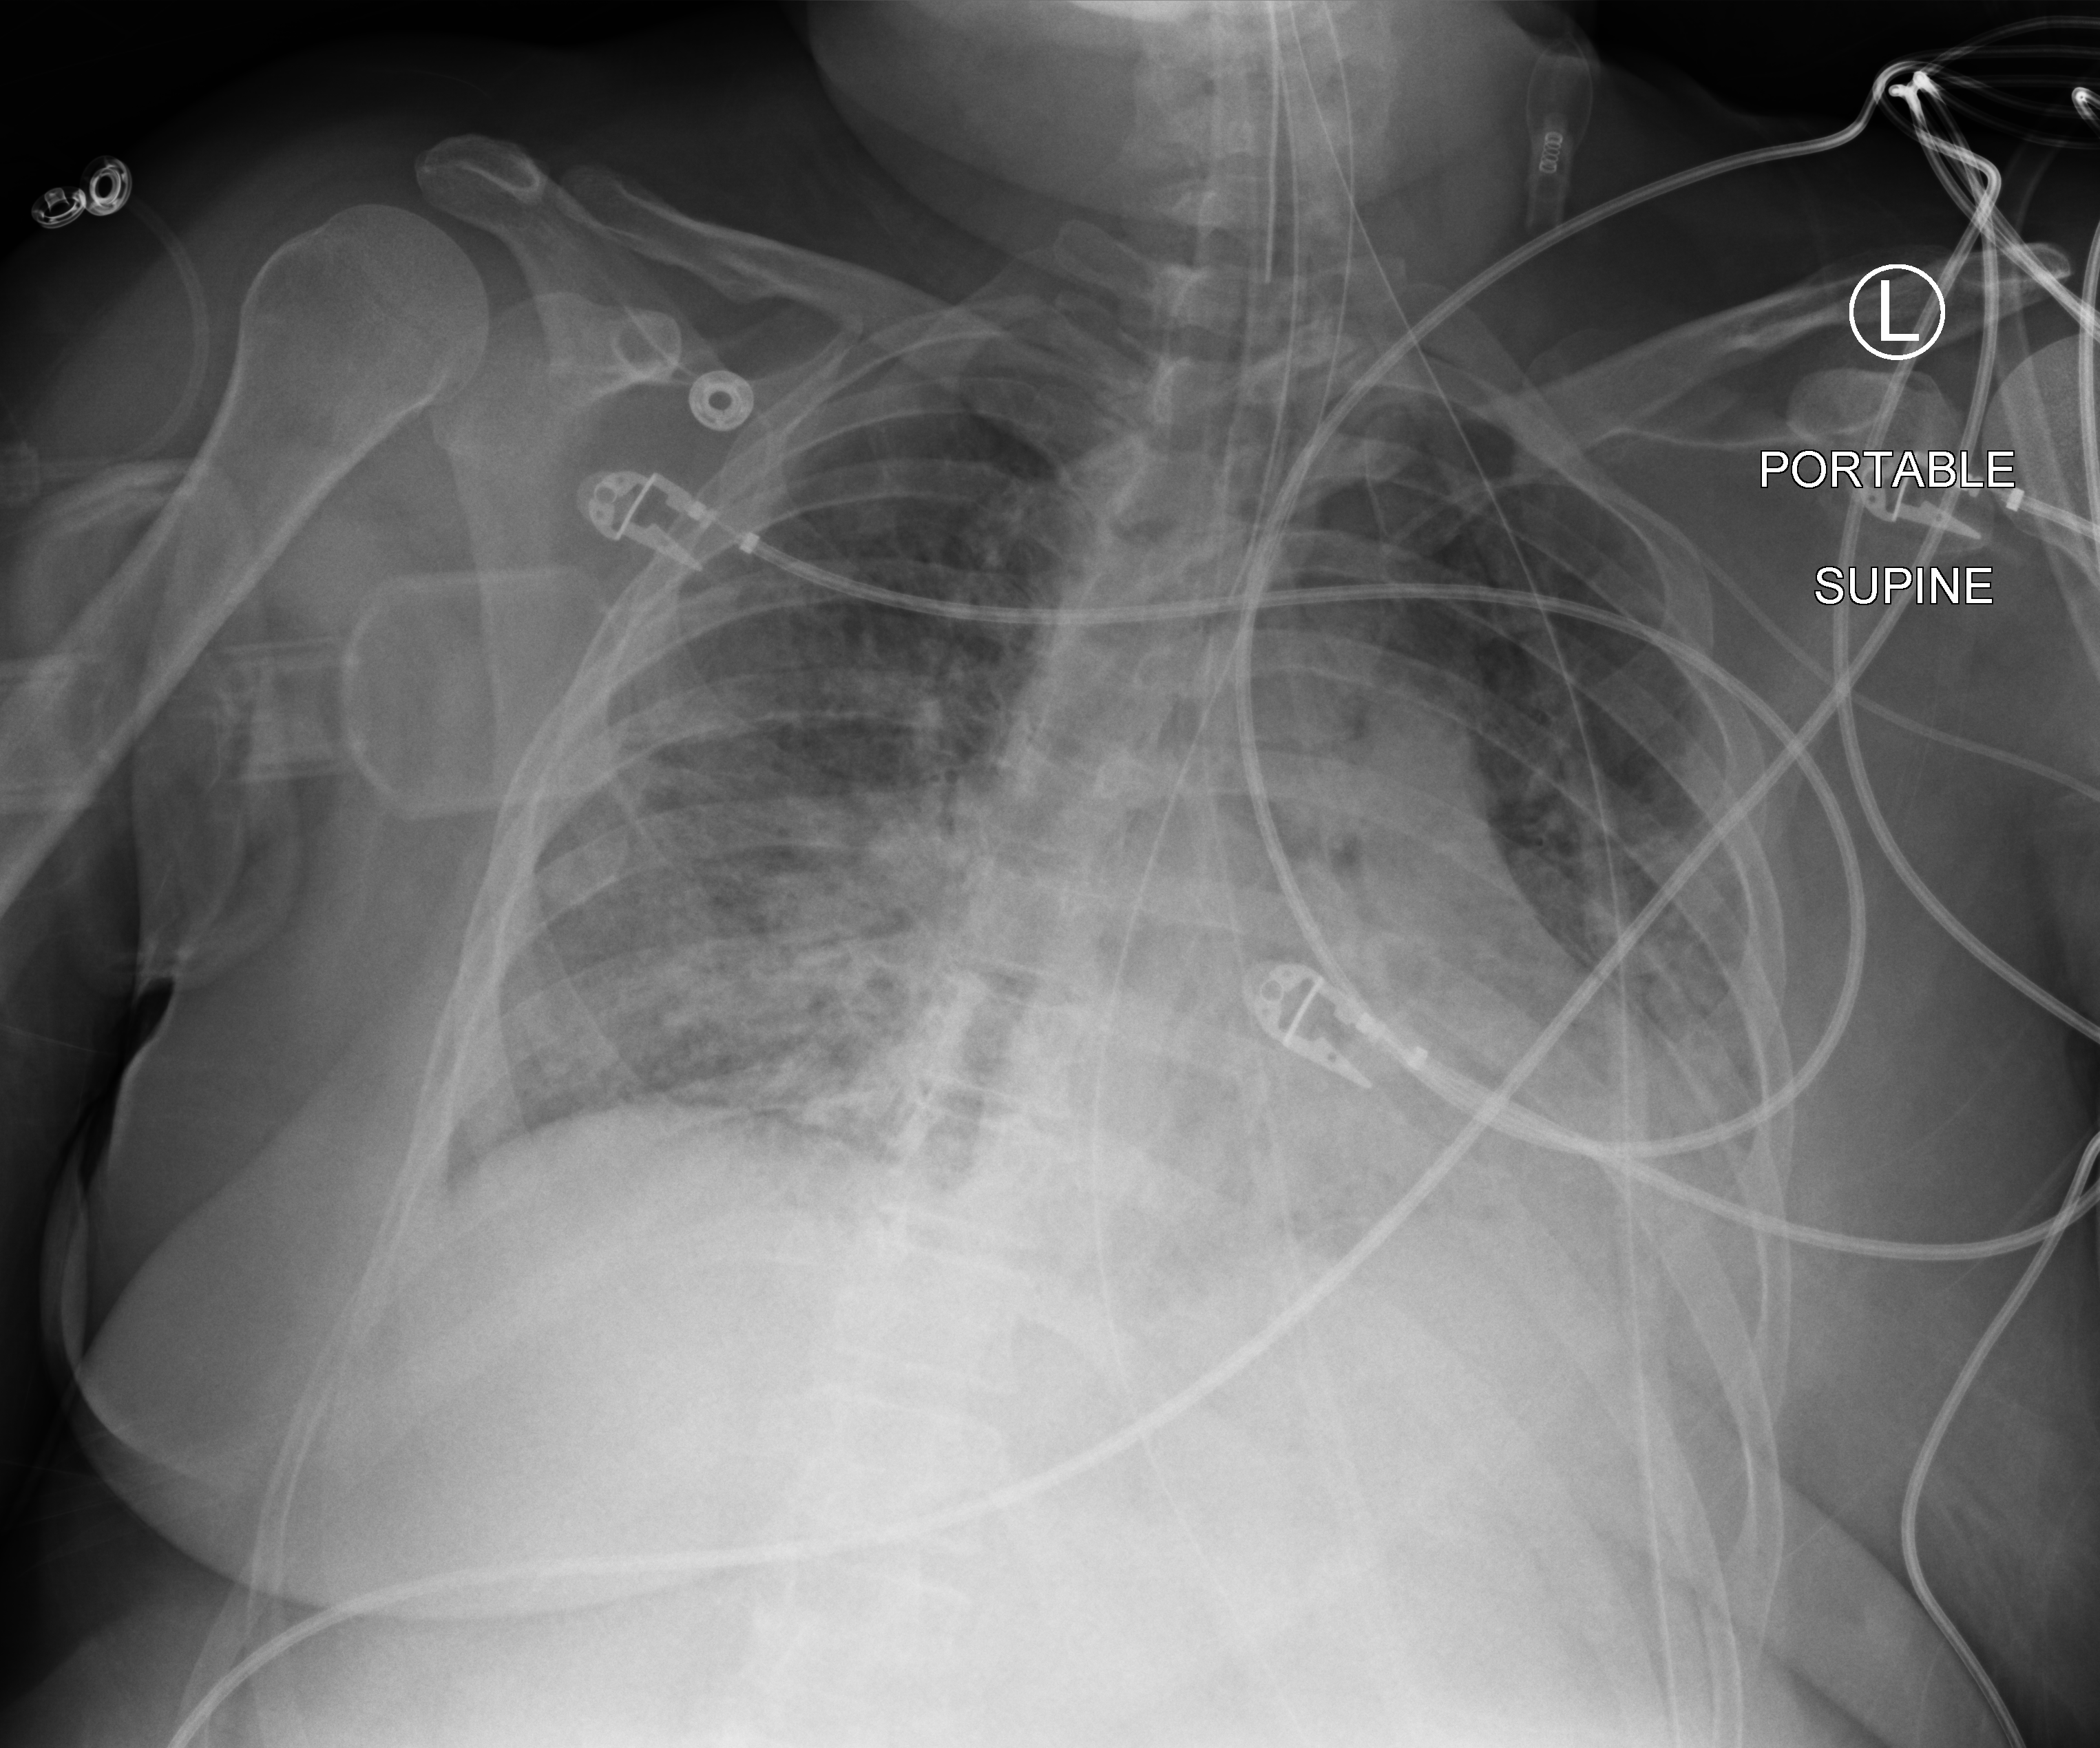
Chest X-ray (portable); anteroposterior (AP) projection. Patient hospitalised with COVID-19; female, aged 18–59 years.
From the hospital-stay record, not from the radiograph (when in the stay this image was taken is not recorded):
- admitted to intensive care during this hospital stay: yes